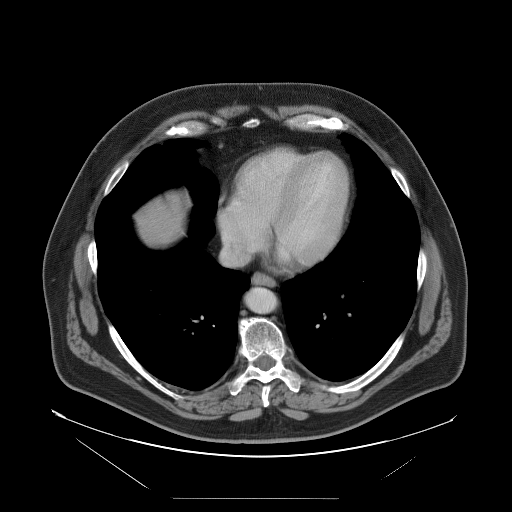
Contrast-enhanced abdominal CT, one axial slice. Slice 99 of 114 in the series (ordered by position). Soft-tissue window (W 400 / L 40 HU). 512 × 512 image matrix. Male patient, age 61 years. Case-level facts recorded for this patient, not image findings: diagnosis: colorectal cancer liver metastases, imaged before liver resection; multiple liver metastases: no; largest metastasis: 6.5 cm; disease in both lobes: yes.
Annotated regions visible in this slice (expert manual segmentation):
- hepatic veins: box from (x=221, y=214) to (x=268, y=266) px
- liver: (x=136, y=203)–(x=185, y=248)